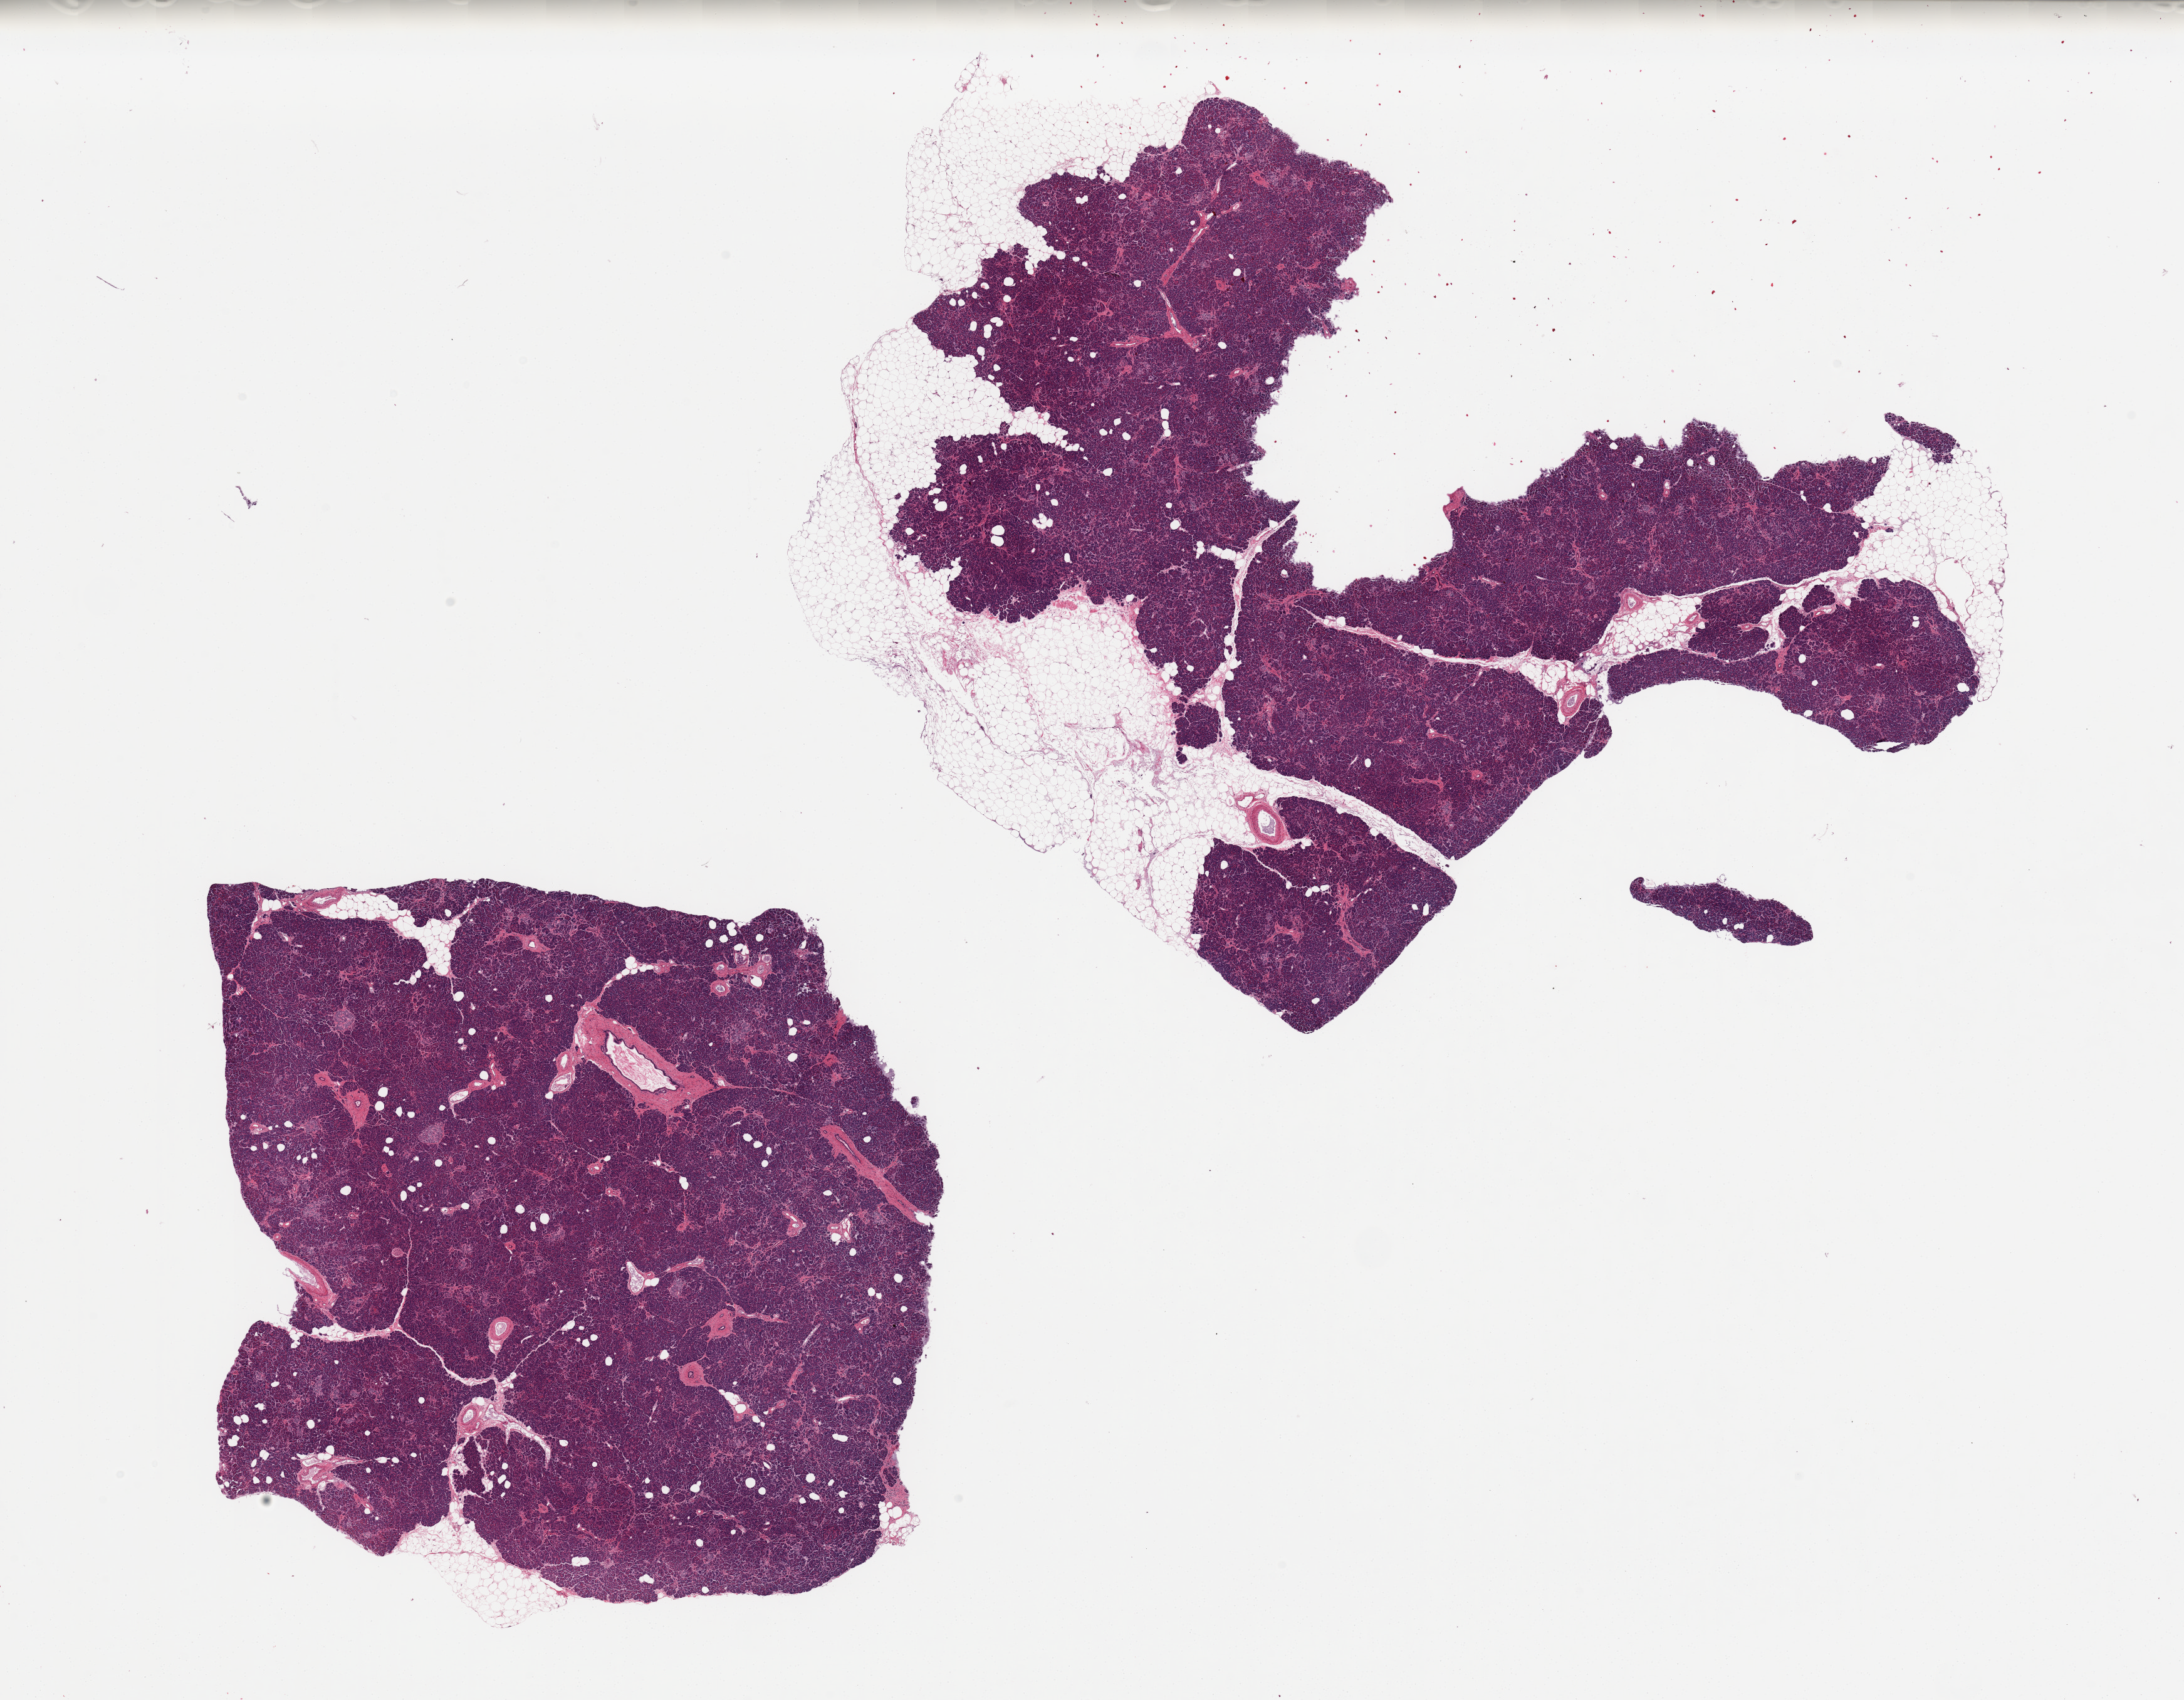
Digitized haematoxylin and eosin-stained section, brightfield — shown as a low-resolution overview of the whole scanned area (about 27.6 x 21.5 mm, acquisition: 20x scan), PAXgene-fixed, paraffin-embedded tissue, sampled site (target tissue): pancreas, tissue donor sample. Donor: female.
Reviewer comment on this tissue sample: 2 pieces, one about 30% fat, increased interstitial fibrosis.